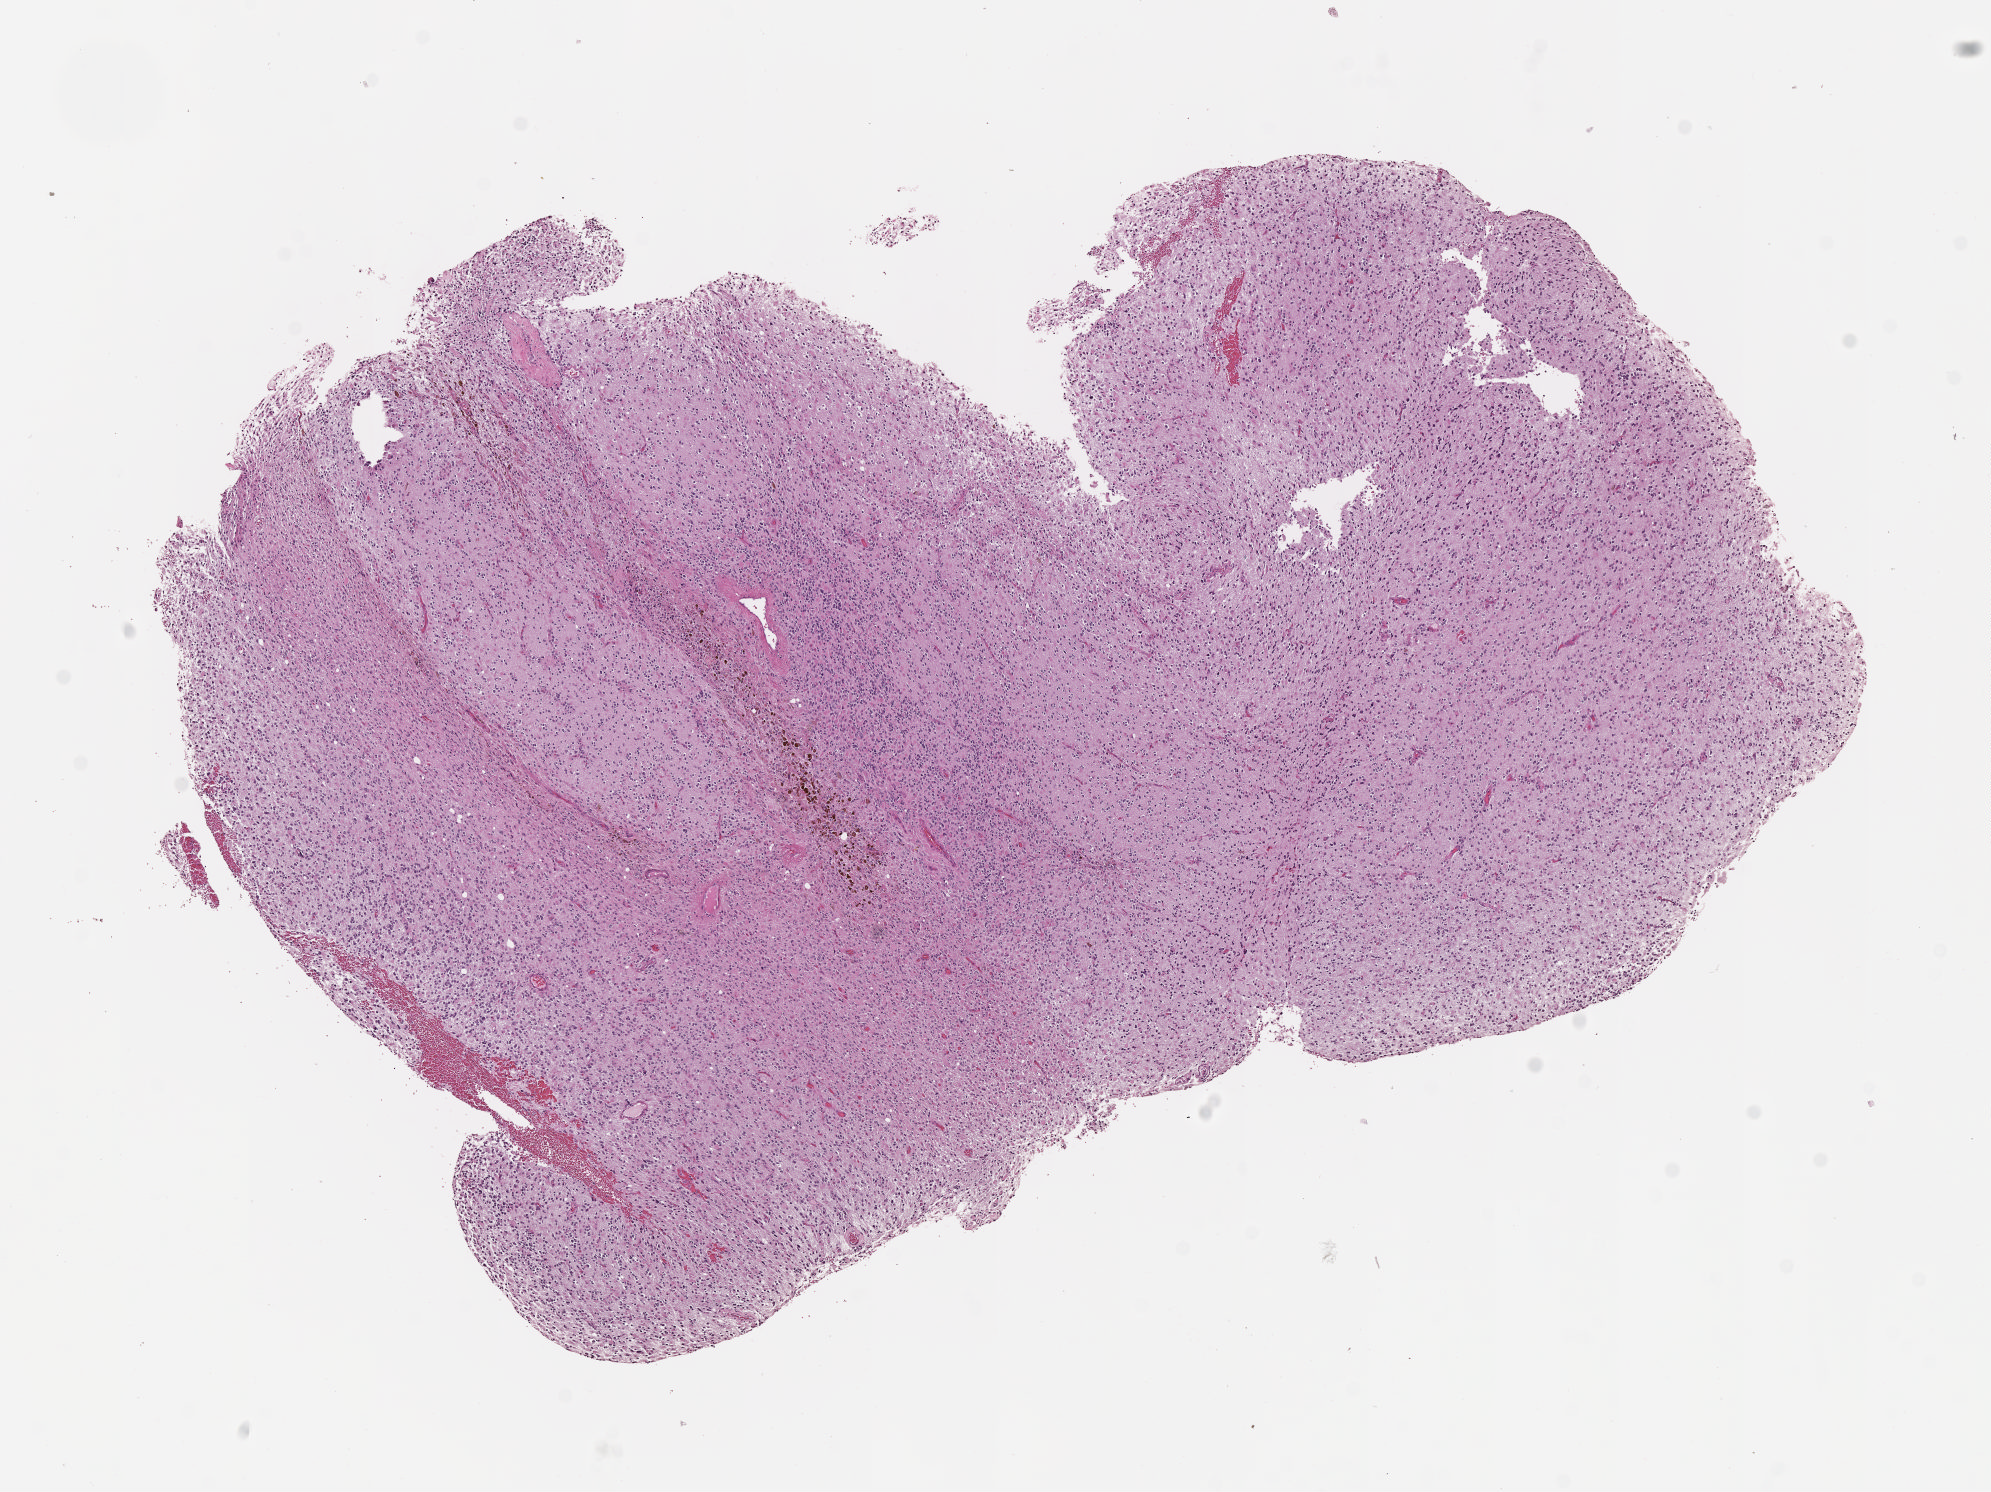
Whole-slide histology image, H&E, low-resolution overview of the scanned area, about 8.1 x 6.0 mm (acquisition: 40x scan), formalin-fixed paraffin-embedded (FFPE) diagnostic section, sample: primary tumour, brain. Female, age 62 years at initial diagnosis. Histologic grade: G2 (moderately differentiated).
* histologic diagnosis: Astrocytoma, NOS